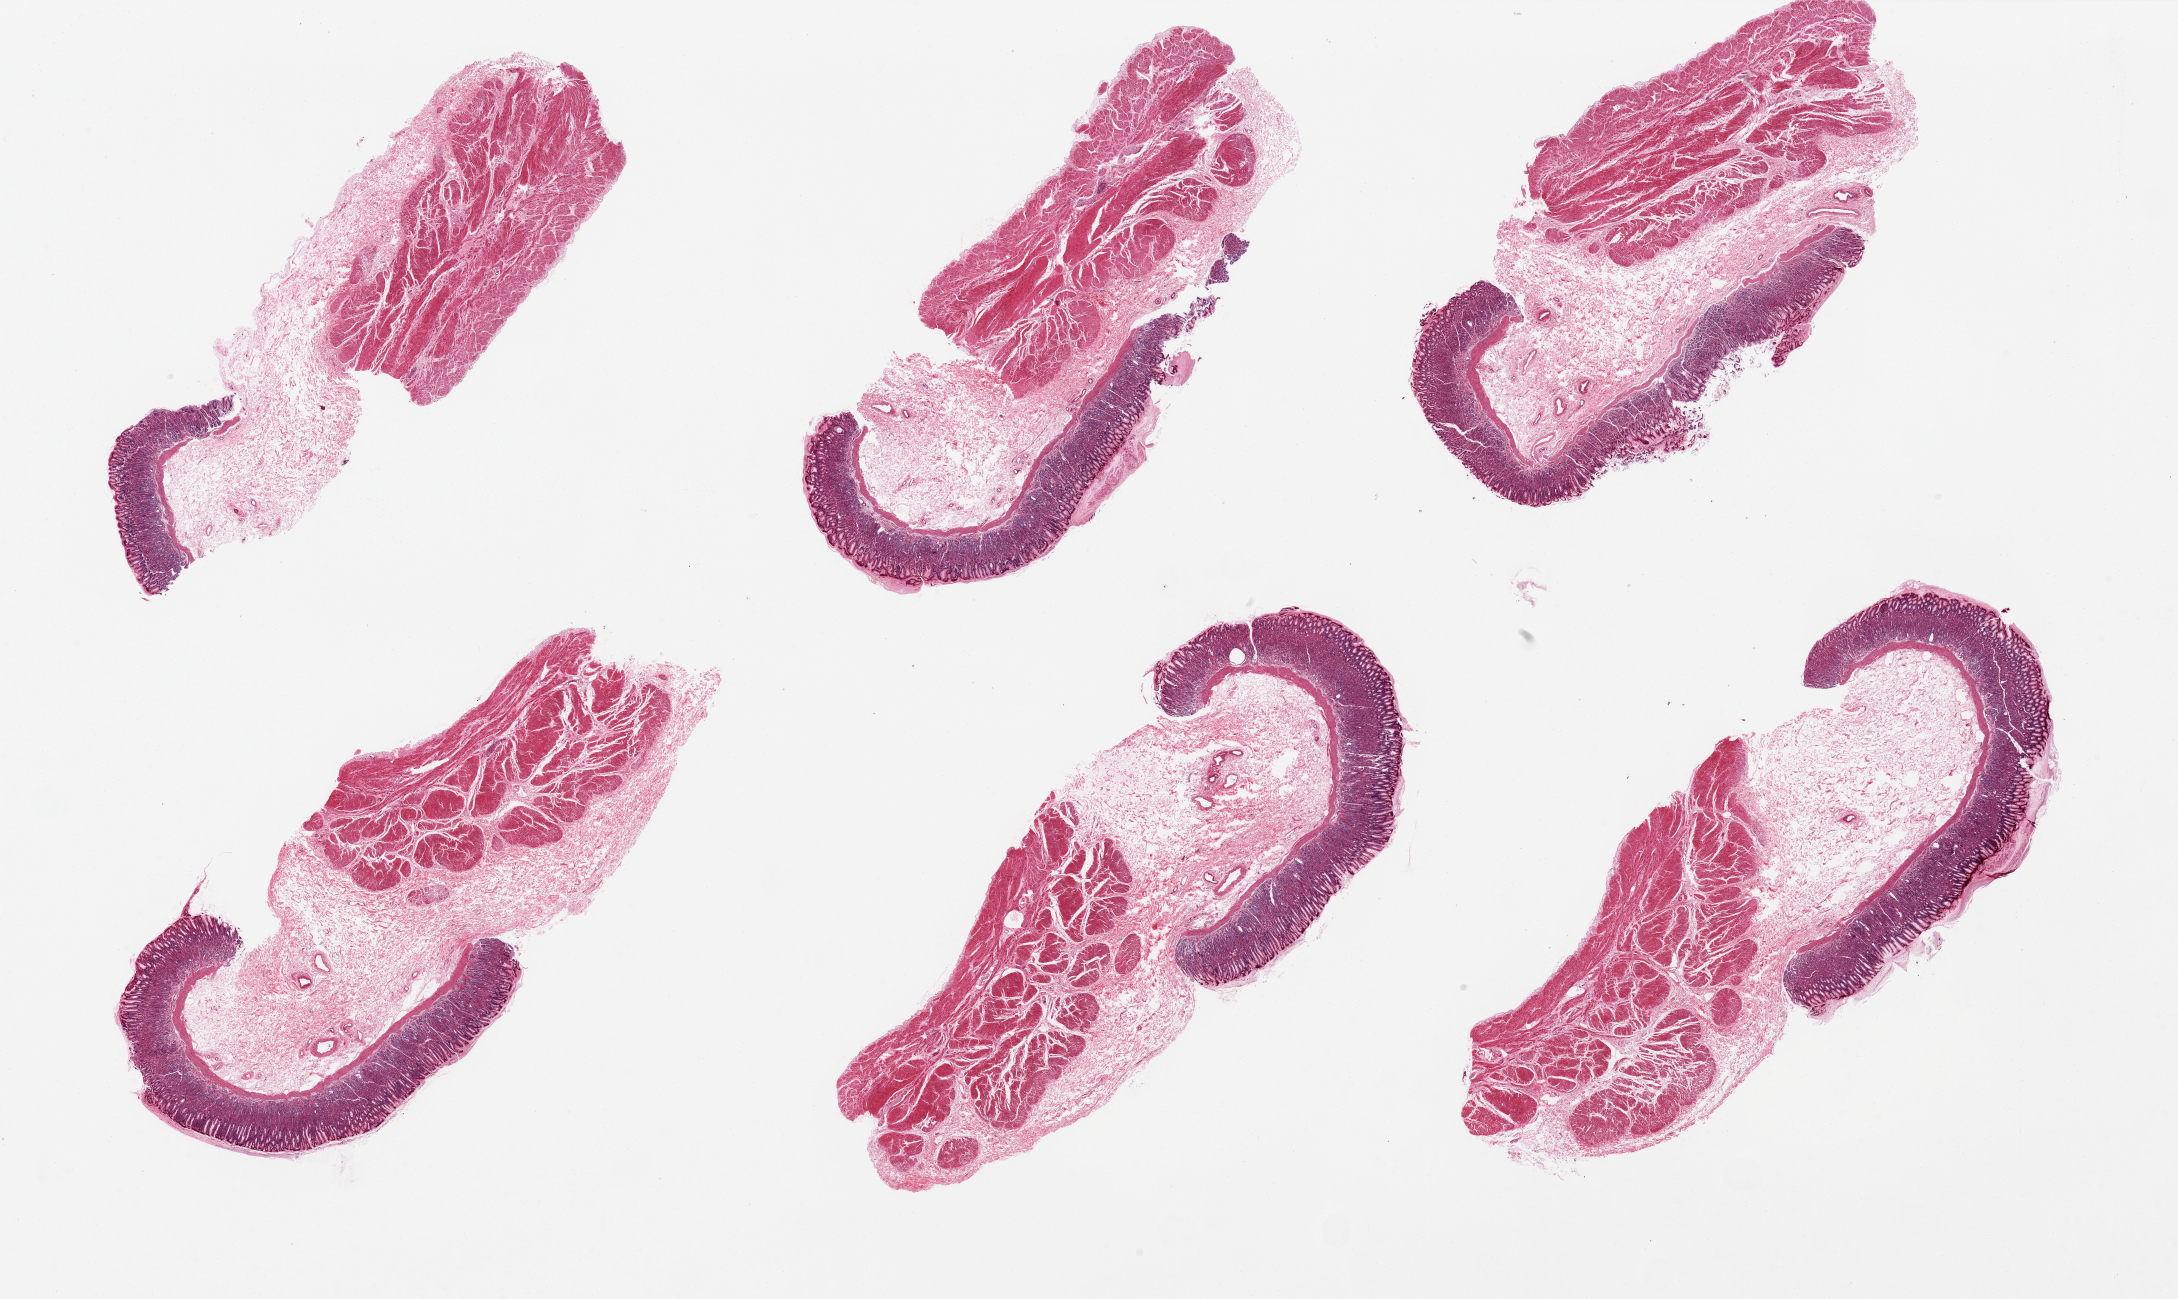
Digitized haematoxylin and eosin-stained section, low-resolution overview of the scanned area, about 34.5 x 20.5 mm; PAXgene-fixed, paraffin-embedded tissue; section of stomach (target tissue); tissue donor sample. Male donor.
- review note (as recorded): 6 pieces, all full thickness